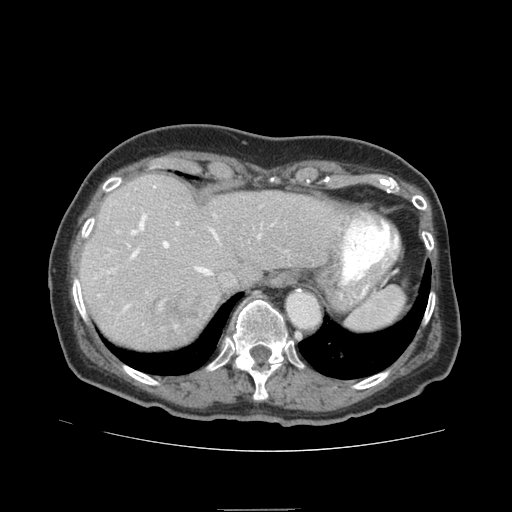
Contrast-enhanced abdominal CT (liver protocol), one axial slice. Position 65 of 95 along the scan axis. Soft-tissue window (W 400 / L 40 HU). 2.5 mm slice thickness. 512 × 512 image matrix, field of view 360 × 360 mm. Case-level facts recorded for this patient, not image findings: diagnosis: hepatocellular carcinoma (patient treated with transarterial chemoembolisation; whether this scan precedes or follows treatment is not stated here); TNM stage (as recorded): Stage-IVA; Child-Pugh class: B.
Structures marked on this image (semi-automatically segmented with operator editing):
- liver parenchyma outside the tumour (the mass and vessels are separate outlines, so this box may not span the whole liver): bounding box <80,174,344,348> (left, top, right, bottom; pixels)
- mass: <142,287,203,335>
- liver vessels: <108,186,273,311>